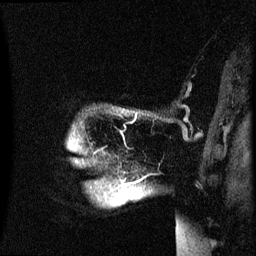
Breast MRI (dynamic contrast-enhanced), one sagittal slice. Position 58 of 60 along the scan axis. Dynamic contrast-enhanced series, image 2 of 3 at this slice position (ordered by acquisition). 1.5 T. TE 4.2 ms, TR 8.4 ms. 2.5 mm slice thickness. 256 × 256 image matrix. Patient: female, 49 years.
Outlined on this slice (semi-automatic segmentation, software-assisted and operator-edited):
- analysis volume of interest (the breast-tissue region the enhancement analysis was run in; not a lesion): bounding box [x1, y1, x2, y2] px = [69, 110, 184, 235]
- tumour enhancement mask (voxels above the 70 % enhancement threshold inside the analysis volume of interest): [122, 184, 128, 189]